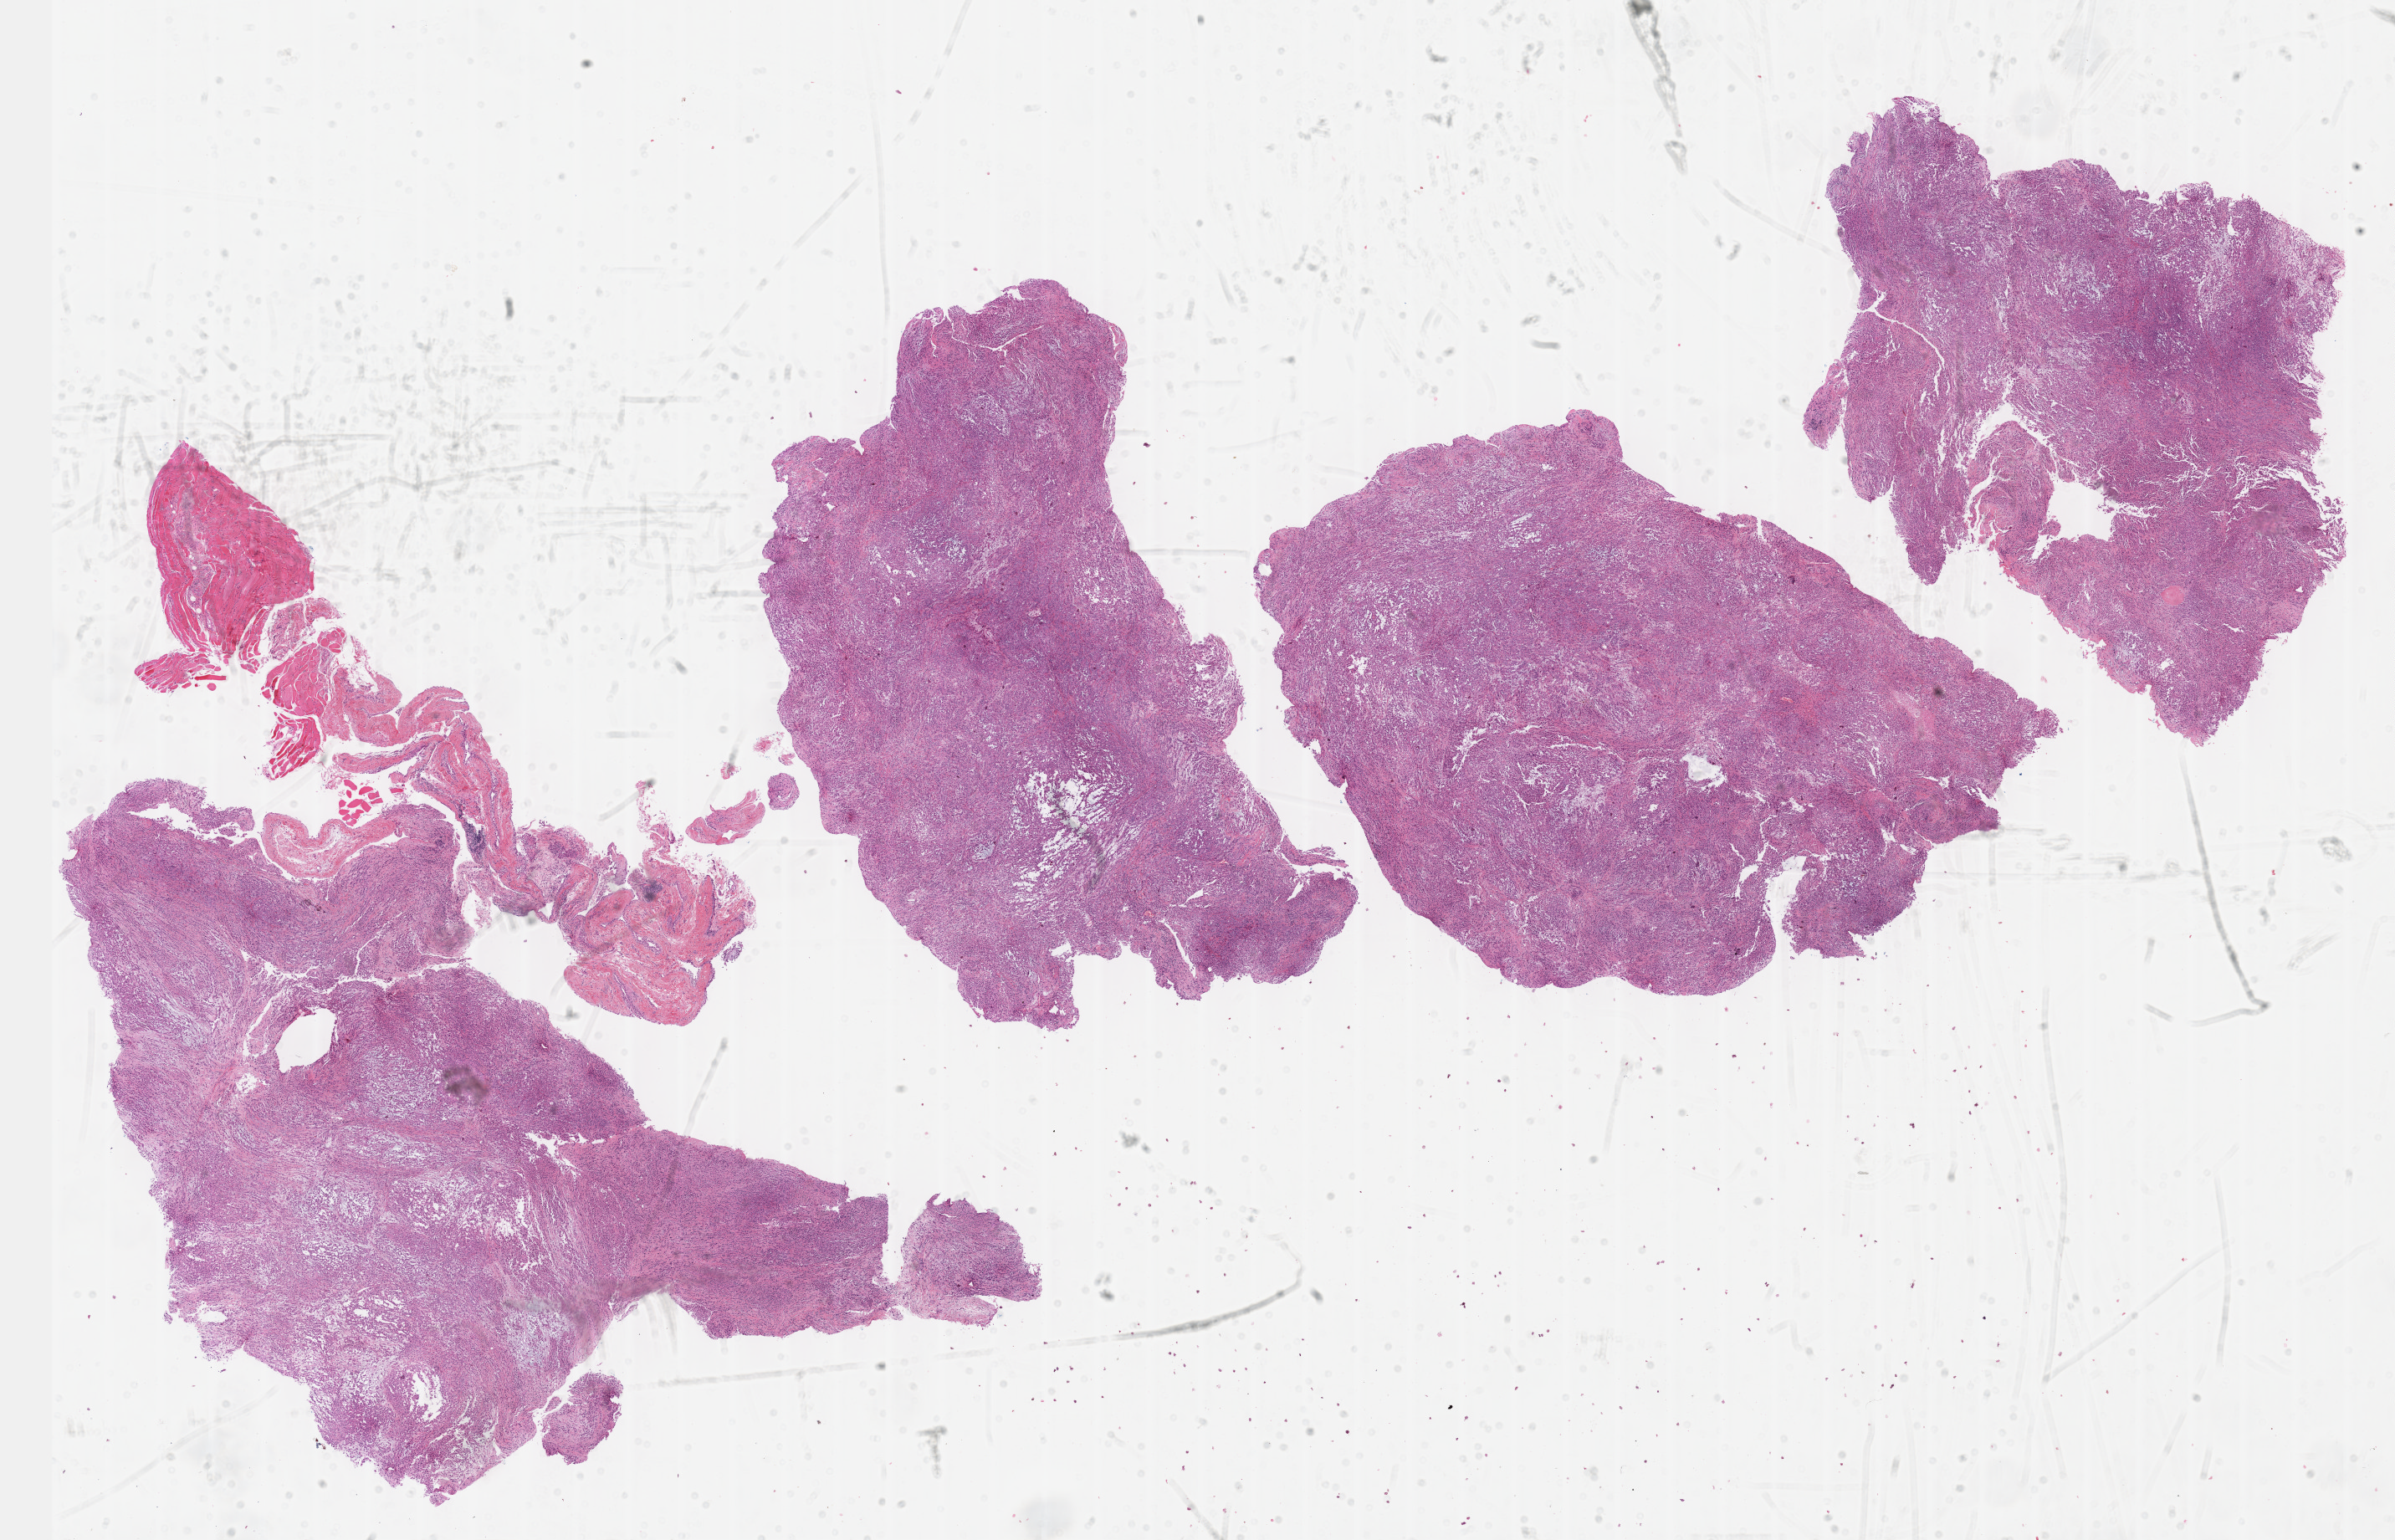
Whole-slide histology image, H&E-stained, a low-resolution overview of the entire scanned area, about 23.1 x 14.9 mm; formalin-fixed paraffin-embedded (FFPE) diagnostic section; mesothelium, primary tumour sample. Male, age 74 years at initial diagnosis.
Histologic diagnosis: Epithelioid mesothelioma, malignant (pleura, NOS). AJCC pathologic stage: I.